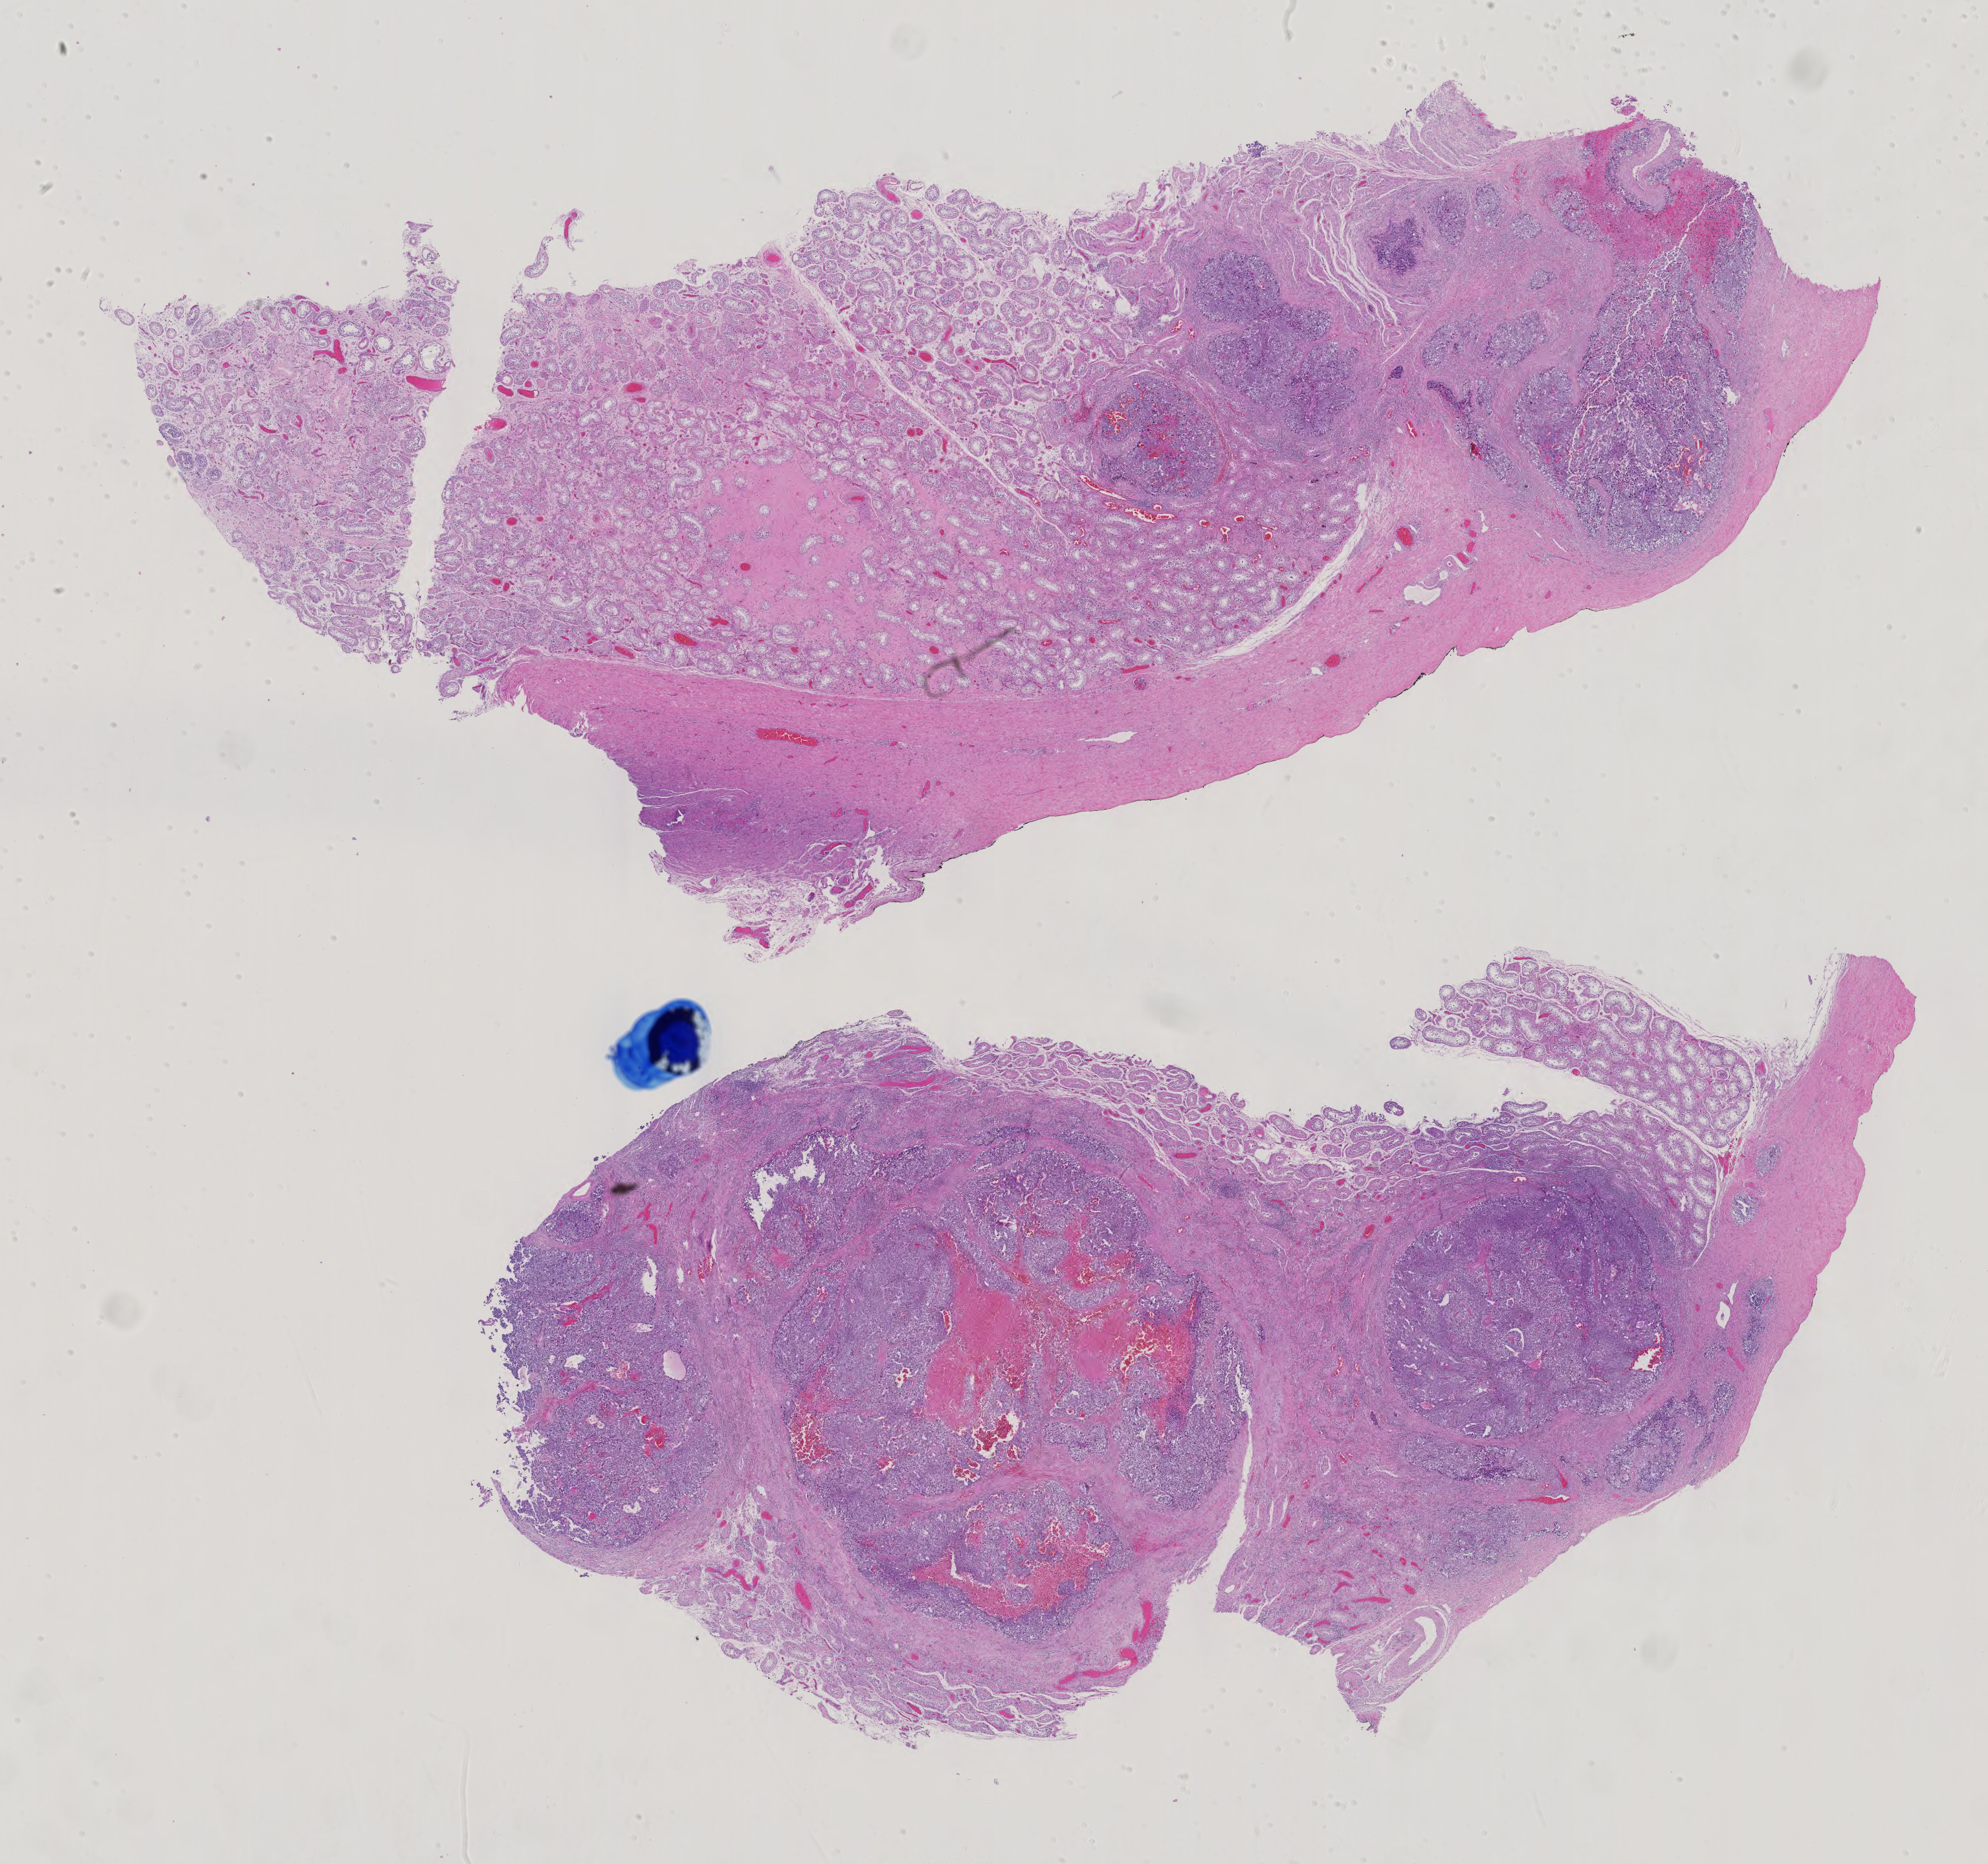
Whole-slide histology image, Hematoxylin and eosin (H&E) stained — shown as a low-resolution overview of the whole scanned area (about 22.4 x 21.0 mm, acquisition: 40x scan); formalin-fixed paraffin-embedded (FFPE) diagnostic section; primary tumour sample from the testis. Patient: male, age at initial diagnosis 33 years.
• laterality: left
• AJCC pathologic stage: IIA (7th edition)
• TNM: T1 N1 M0
• histologic diagnosis: Embryonal carcinoma, NOS